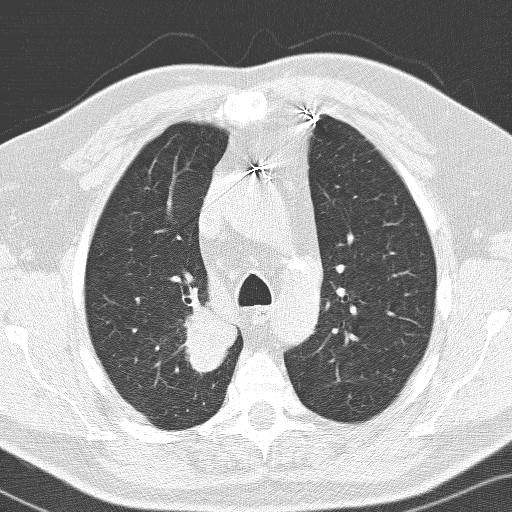
Low-dose screening chest CT, one axial slice; position 106 of 141 along the scan axis; 120 kVp; lung window (W 1500 / L -600 HU); 512 × 512 image matrix, field of view 326 × 326 mm.
Annotated regions visible in this slice (manually delineated by an expert):
- lesion 1 (tumor, upper lobe of right lung): bounding box [x1, y1, x2, y2] px = [185, 297, 237, 374]